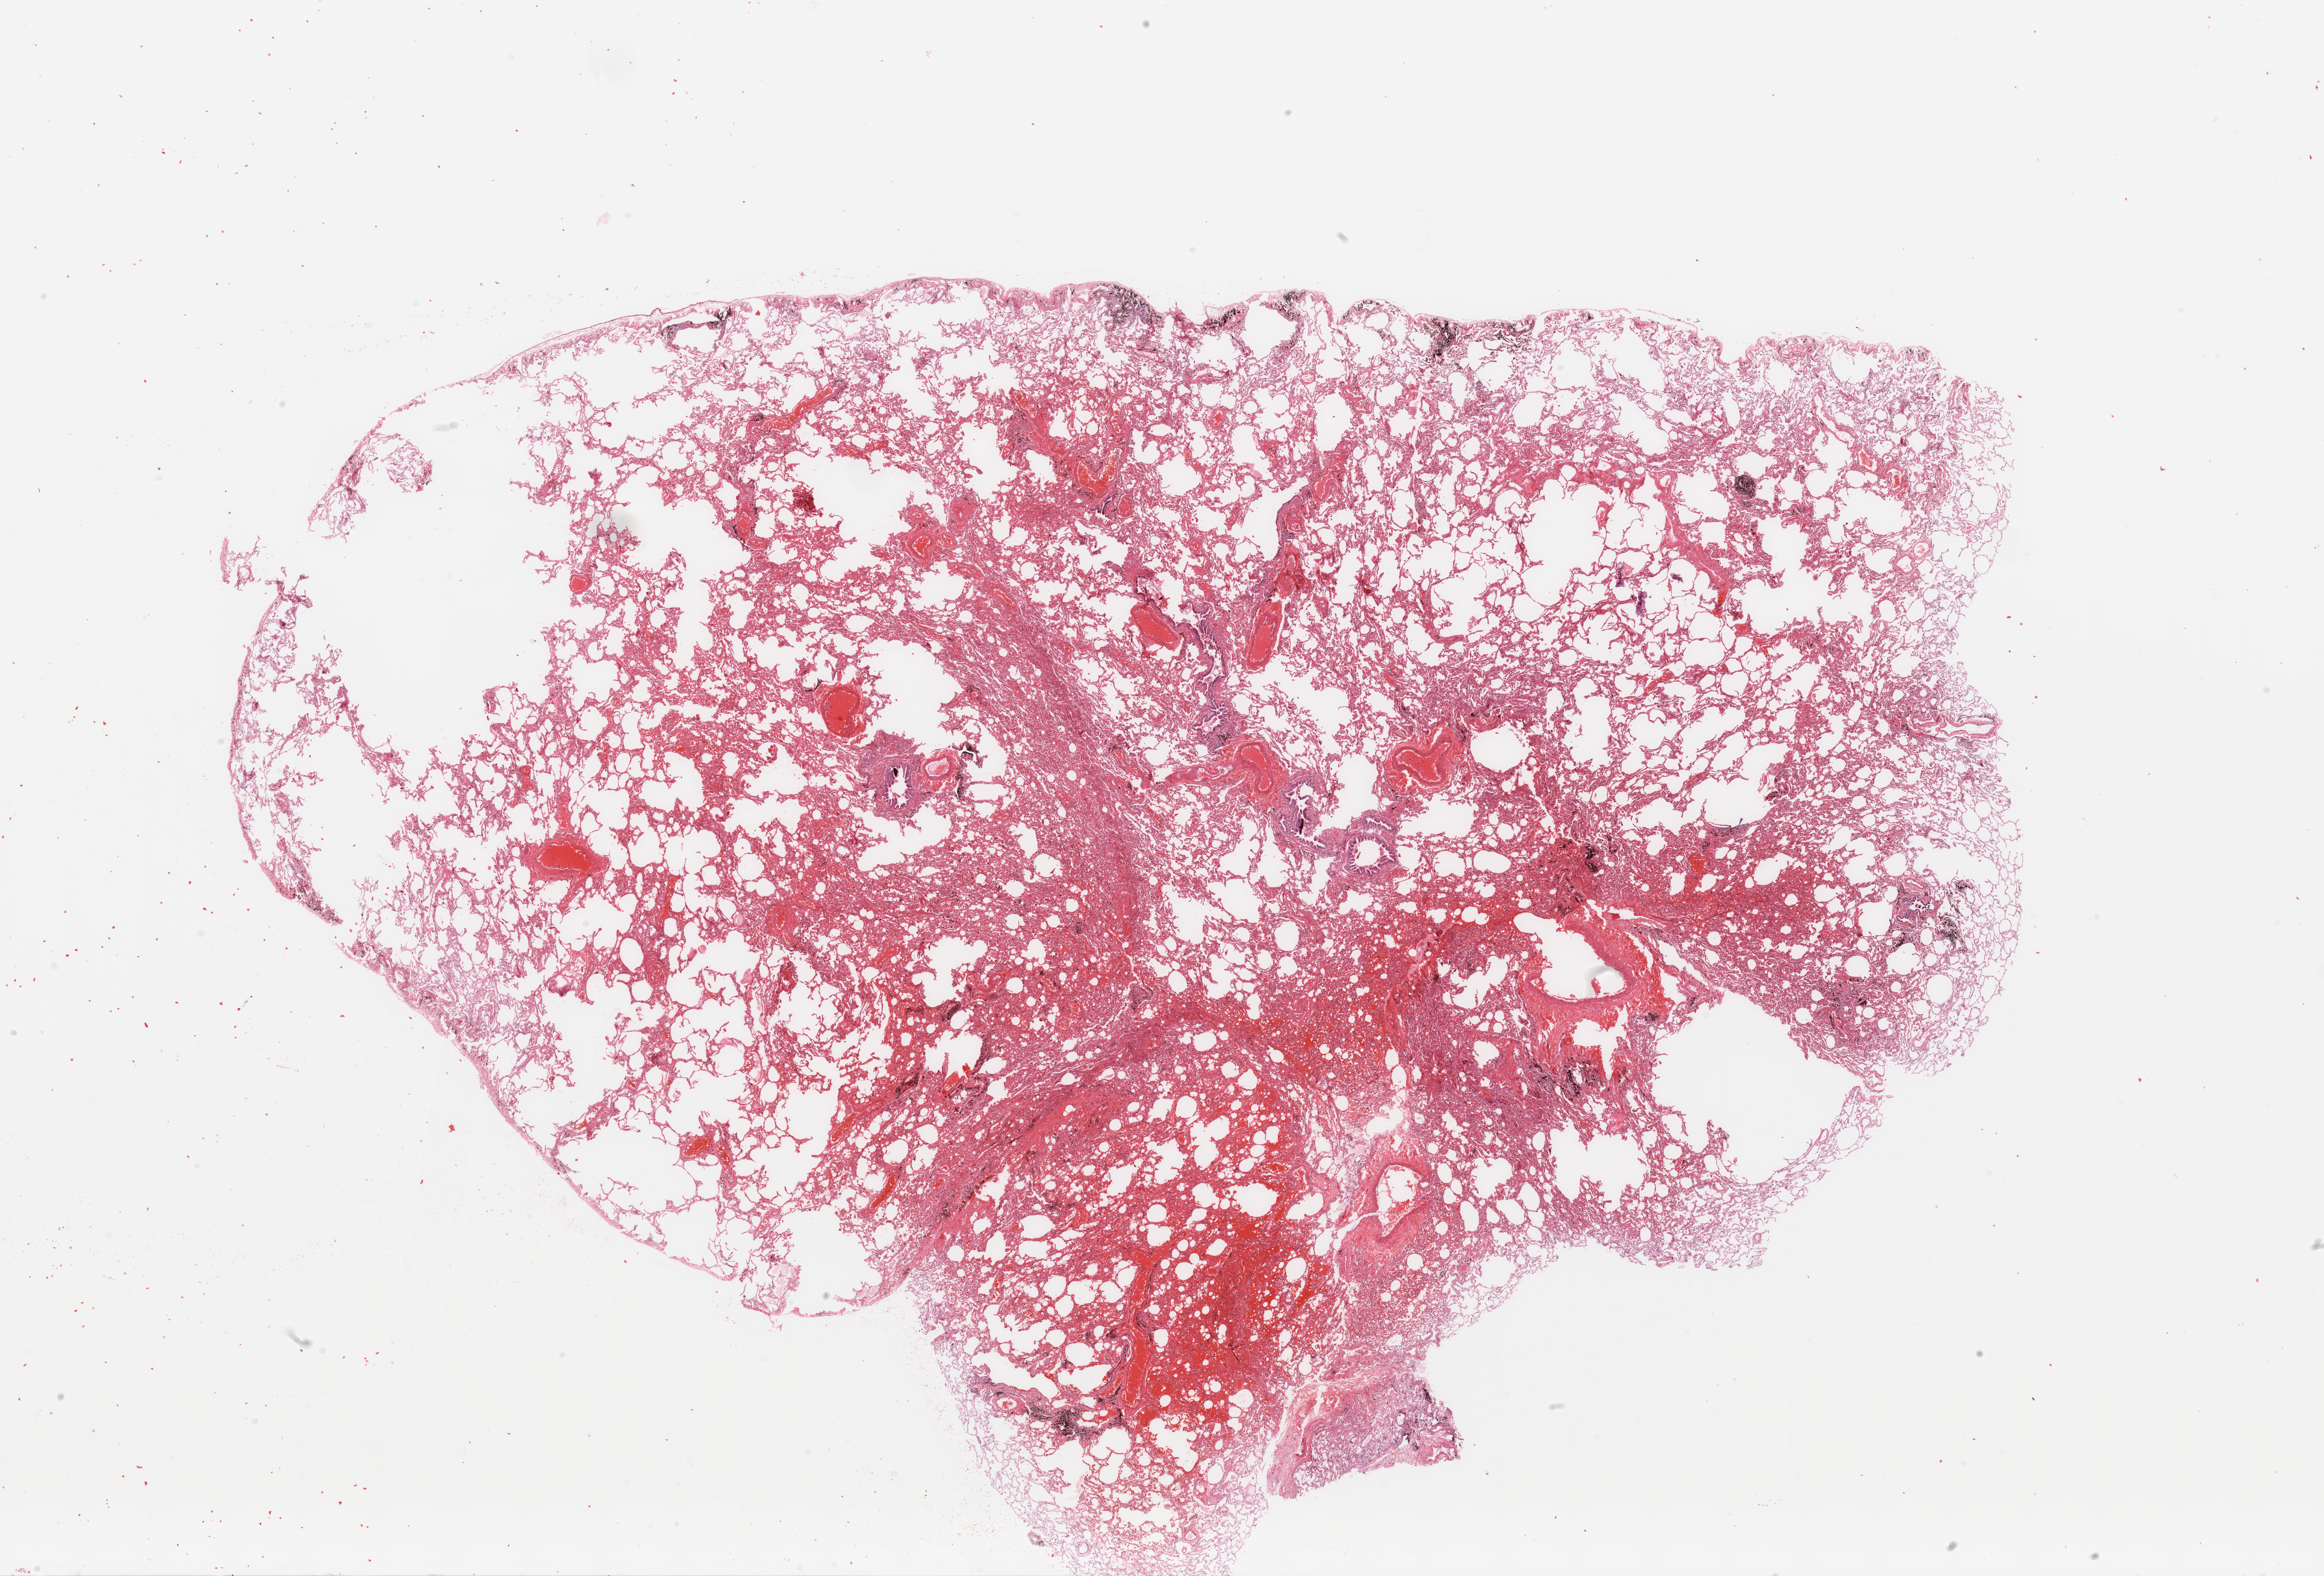
Whole-slide histology image, H&E-stained, shown as a low-resolution overview of the whole scanned area (about 30.5 x 20.7 mm, acquisition: 20x scan); normal (non-tumour) tissue sample, sampled site: lung. Patient: male, age 45 years.
- this section: normal (non-tumour) tissue from the same patient
- patient diagnosis: Adenocarcinoma, NOS